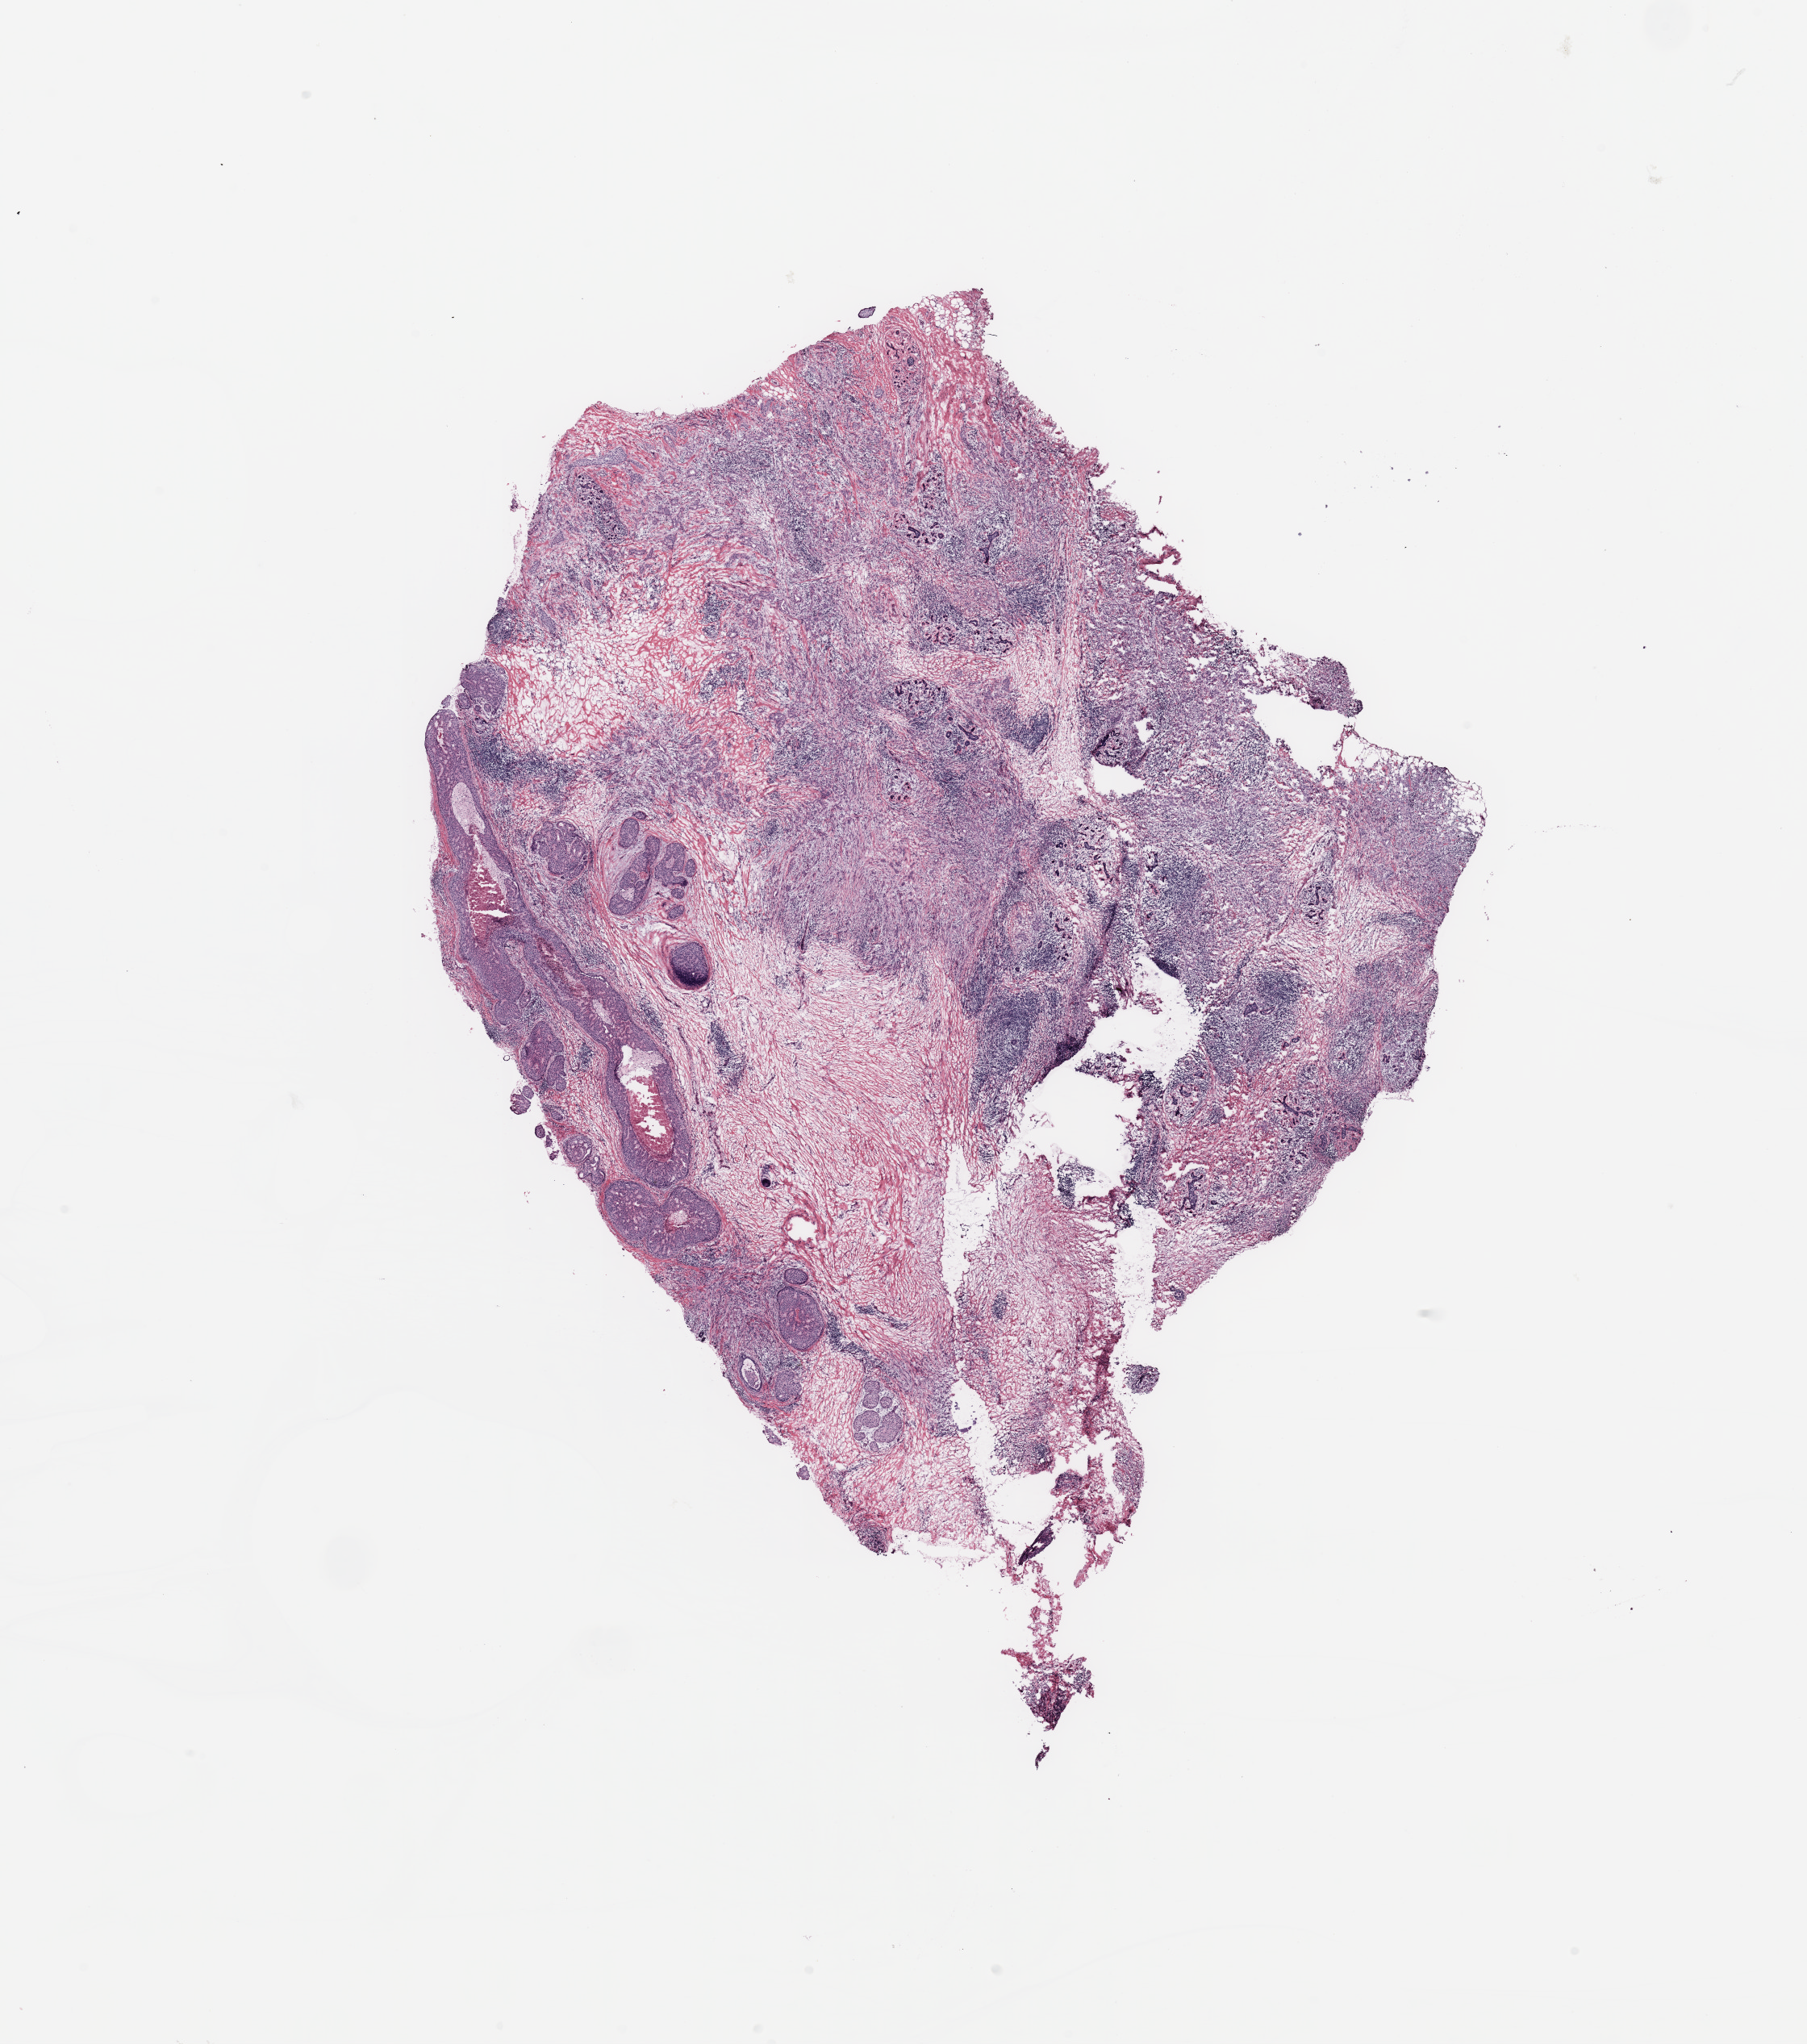
H&E-stained whole-slide image — whole scanned area (about 17.7 x 20.0 mm) shown as a low-resolution overview; breast, tissue type not recorded.
* patient diagnosis (cohort enrolment): breast cancer (breast)